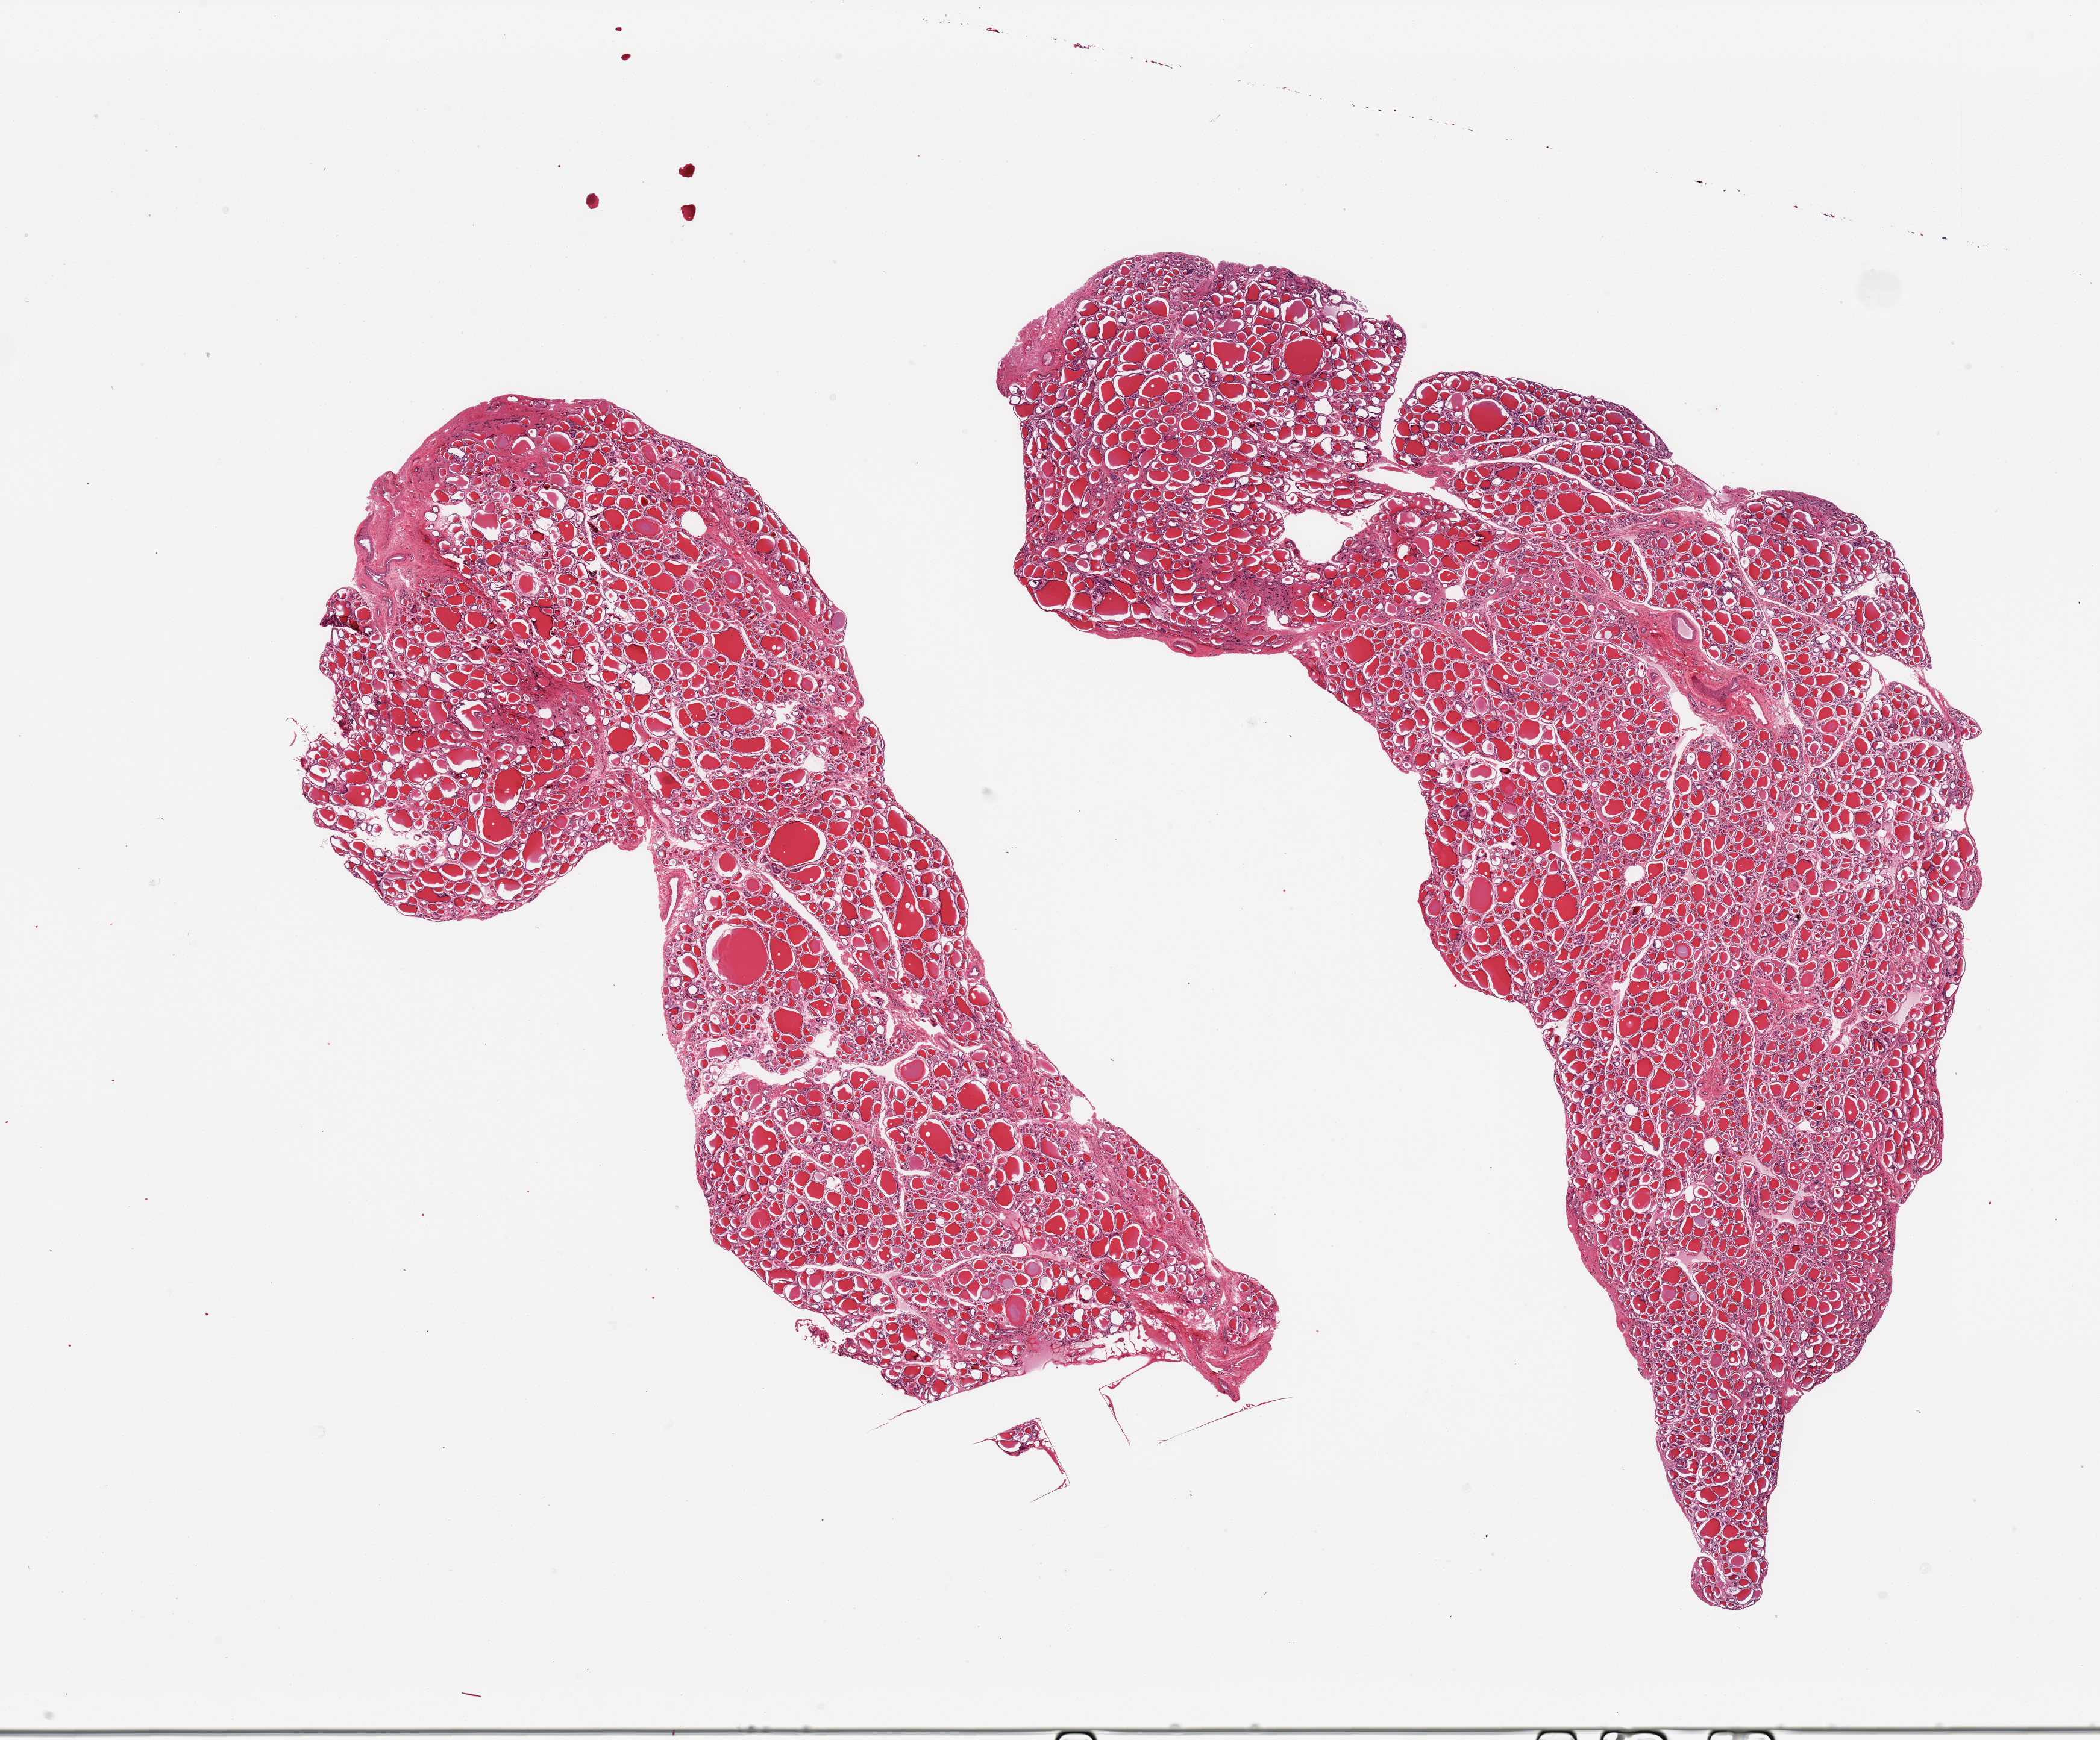
Haematoxylin and eosin whole-slide image, brightfield — low-resolution overview of the scanned area, about 27.6 x 22.8 mm. PAXgene-fixed, paraffin-embedded tissue. Sampled site (target tissue): thyroid. Donor tissue sample. Donor sex: male.
Reviewer comment on this tissue sample: 2 pieces, no abnormalities.